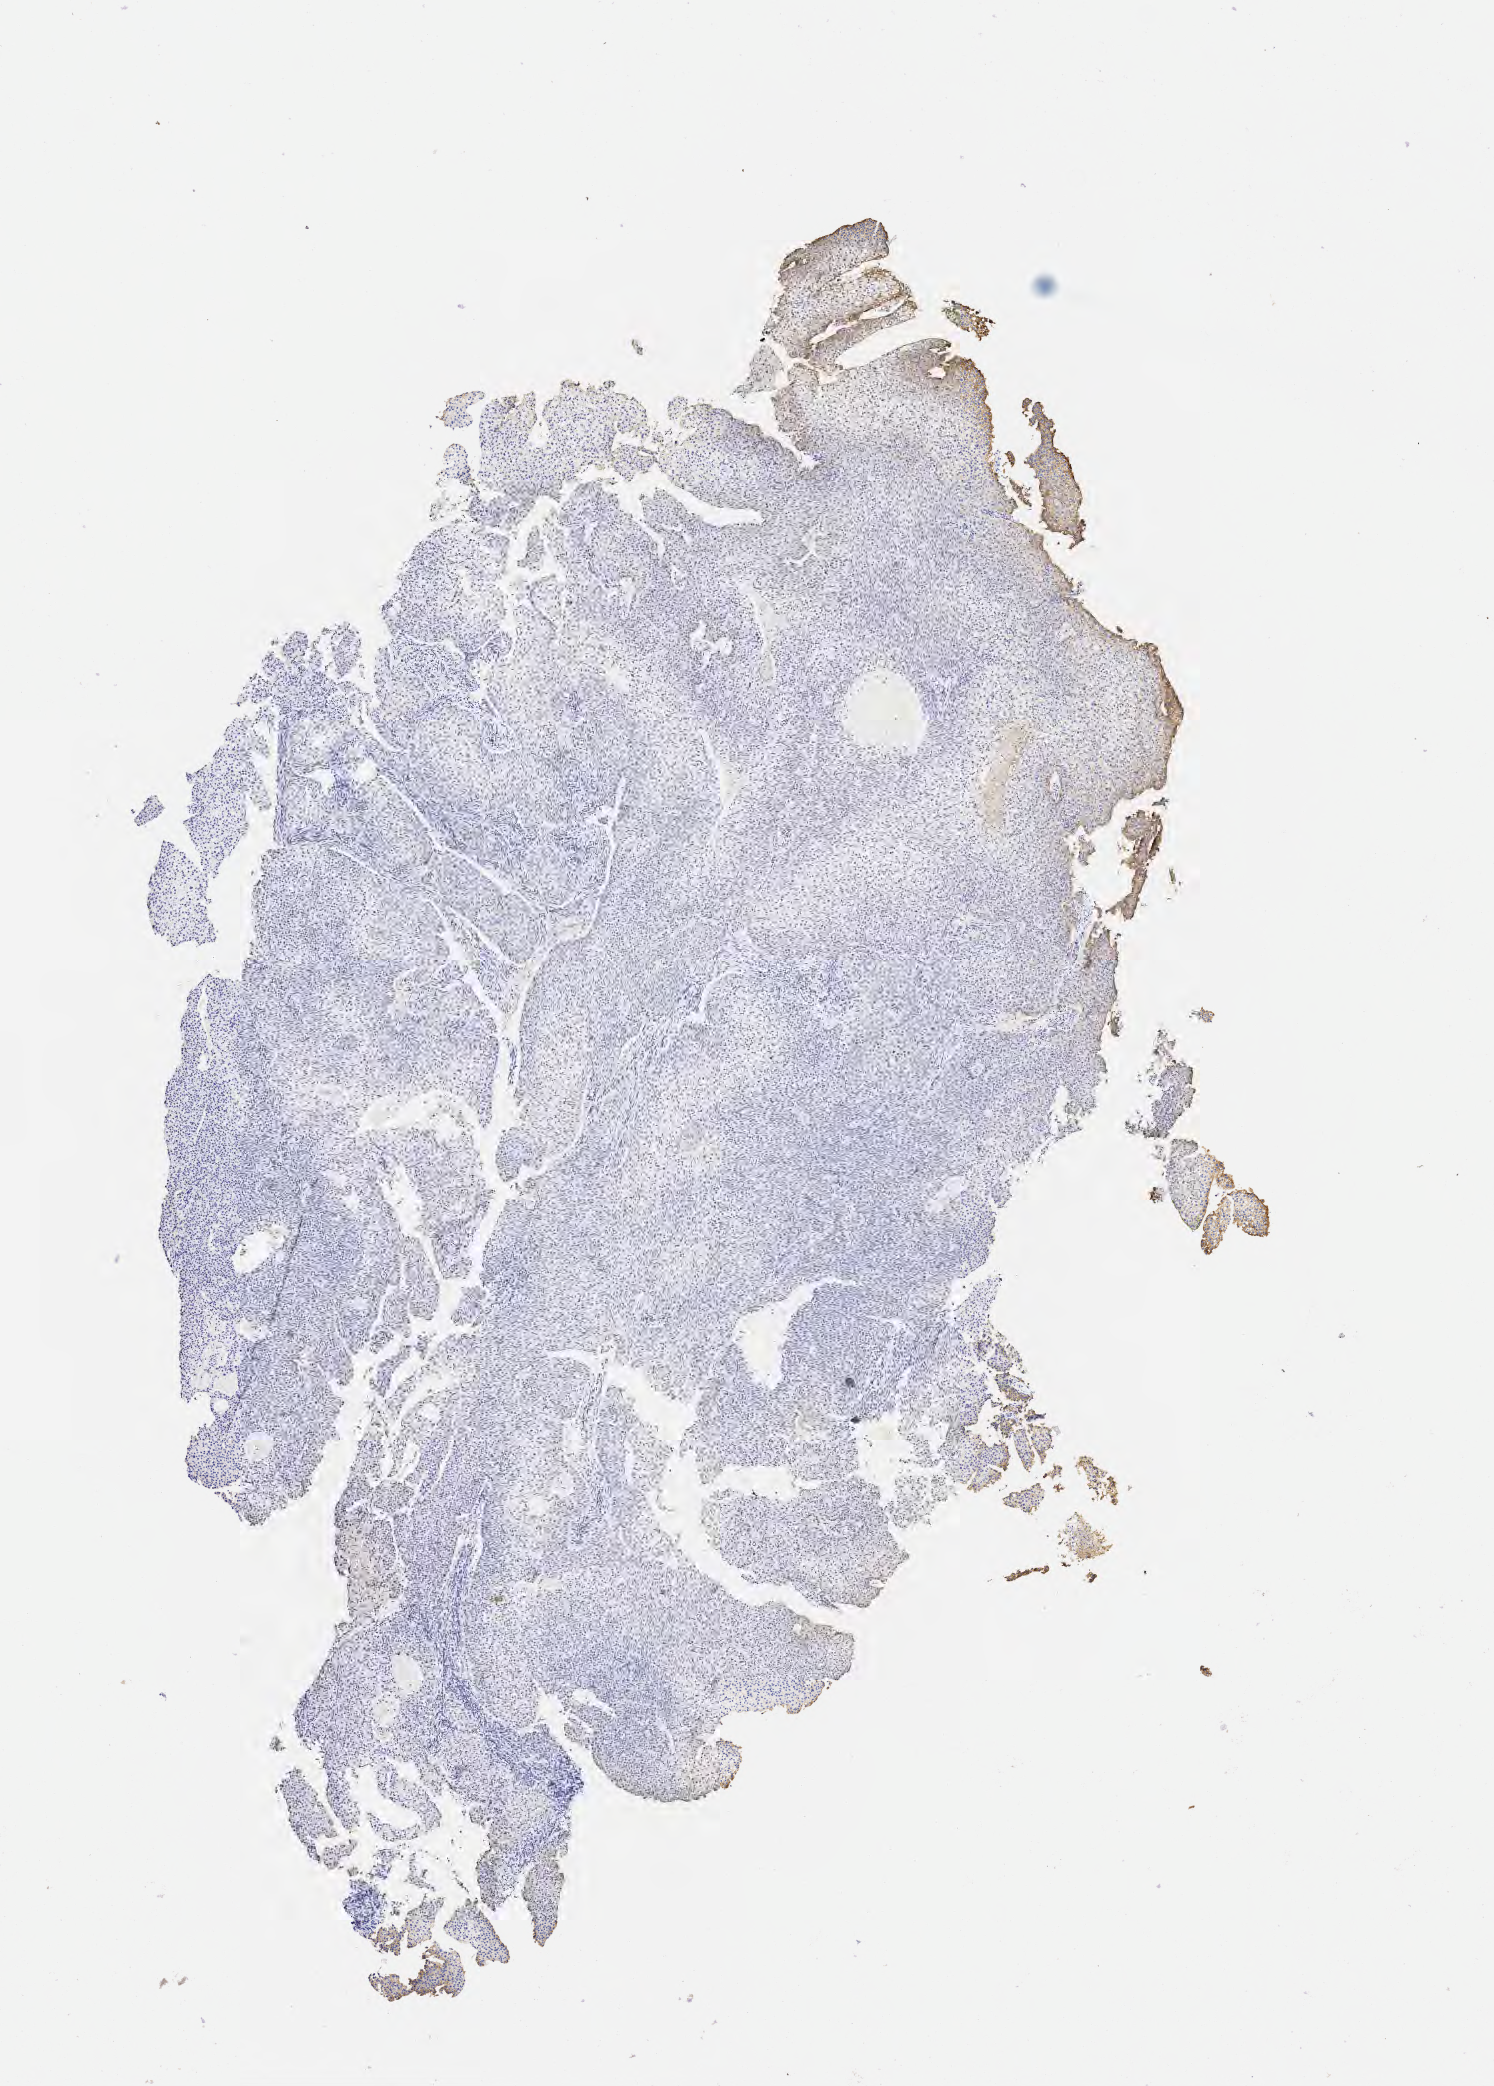
Whole-slide image, immunohistochemical stain for MOC-31 (anti-EpCAM), whole scanned area (about 6.0 x 8.4 mm) shown as a low-resolution overview, tumor tissue, site: cervix. Patient: female, aged 39.
Histologic diagnosis: Squamous cell carcinoma, large cell, nonkeratinizing, NOS.